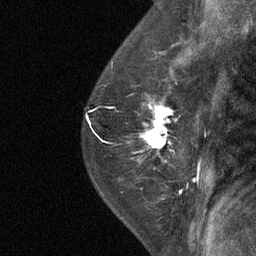
Breast MRI (dynamic contrast-enhanced), one sagittal slice. Slice 46 of 64 in the series (ordered by position). Dynamic contrast-enhanced study with each time point stored as its own series, time point 2 of 4 at this slice position (early post-contrast, ordered by acquisition time). 1.5 T. TE 4.8 ms, TR 27 ms. 2 mm slice thickness. 256 × 256 image matrix. Patient: female, 50 years. From the clinical record (not read from this slice): setting: breast cancer imaged before/during neoadjuvant chemotherapy; receptor status: HER2-positive.
Annotated regions visible in this slice (semi-automatic segmentation, software-assisted and operator-edited):
- analysis volume of interest (the breast-tissue region the enhancement analysis was run in; not a lesion): bounding box [x1, y1, x2, y2] px = [123, 91, 189, 177]
- tumour enhancement mask (voxels above the 90 % enhancement threshold inside the analysis volume of interest): [140, 105, 173, 149]